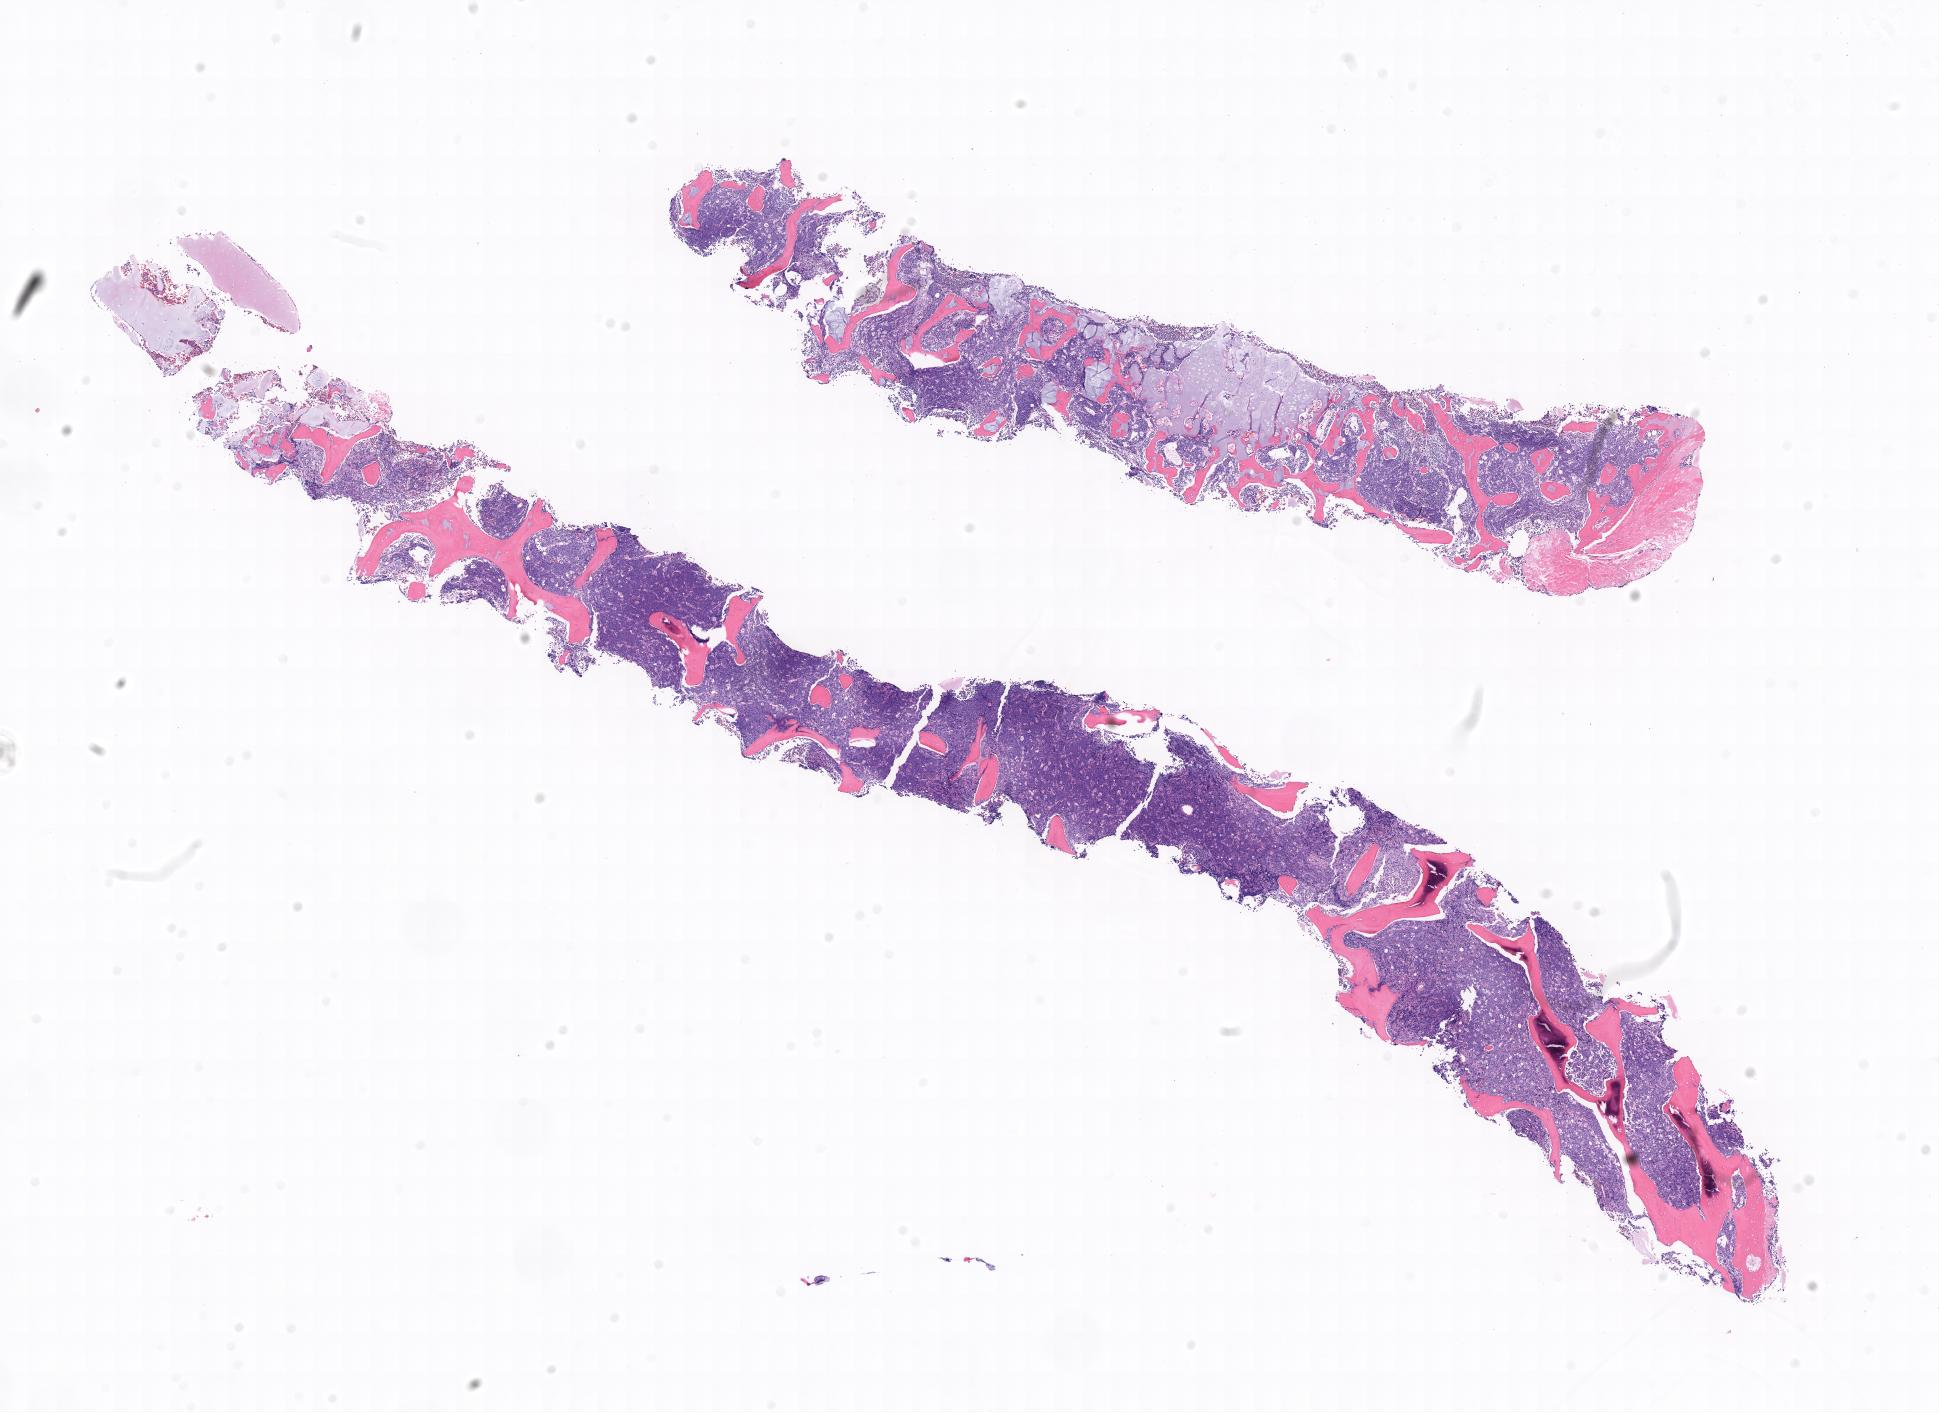
Digitized haematoxylin and eosin-stained section, whole scanned area shown as a low-resolution overview; tumor tissue; site: bone marrow. Patient male; 11 years old.
Histologic diagnosis: Burkitt lymphoma, NOS.